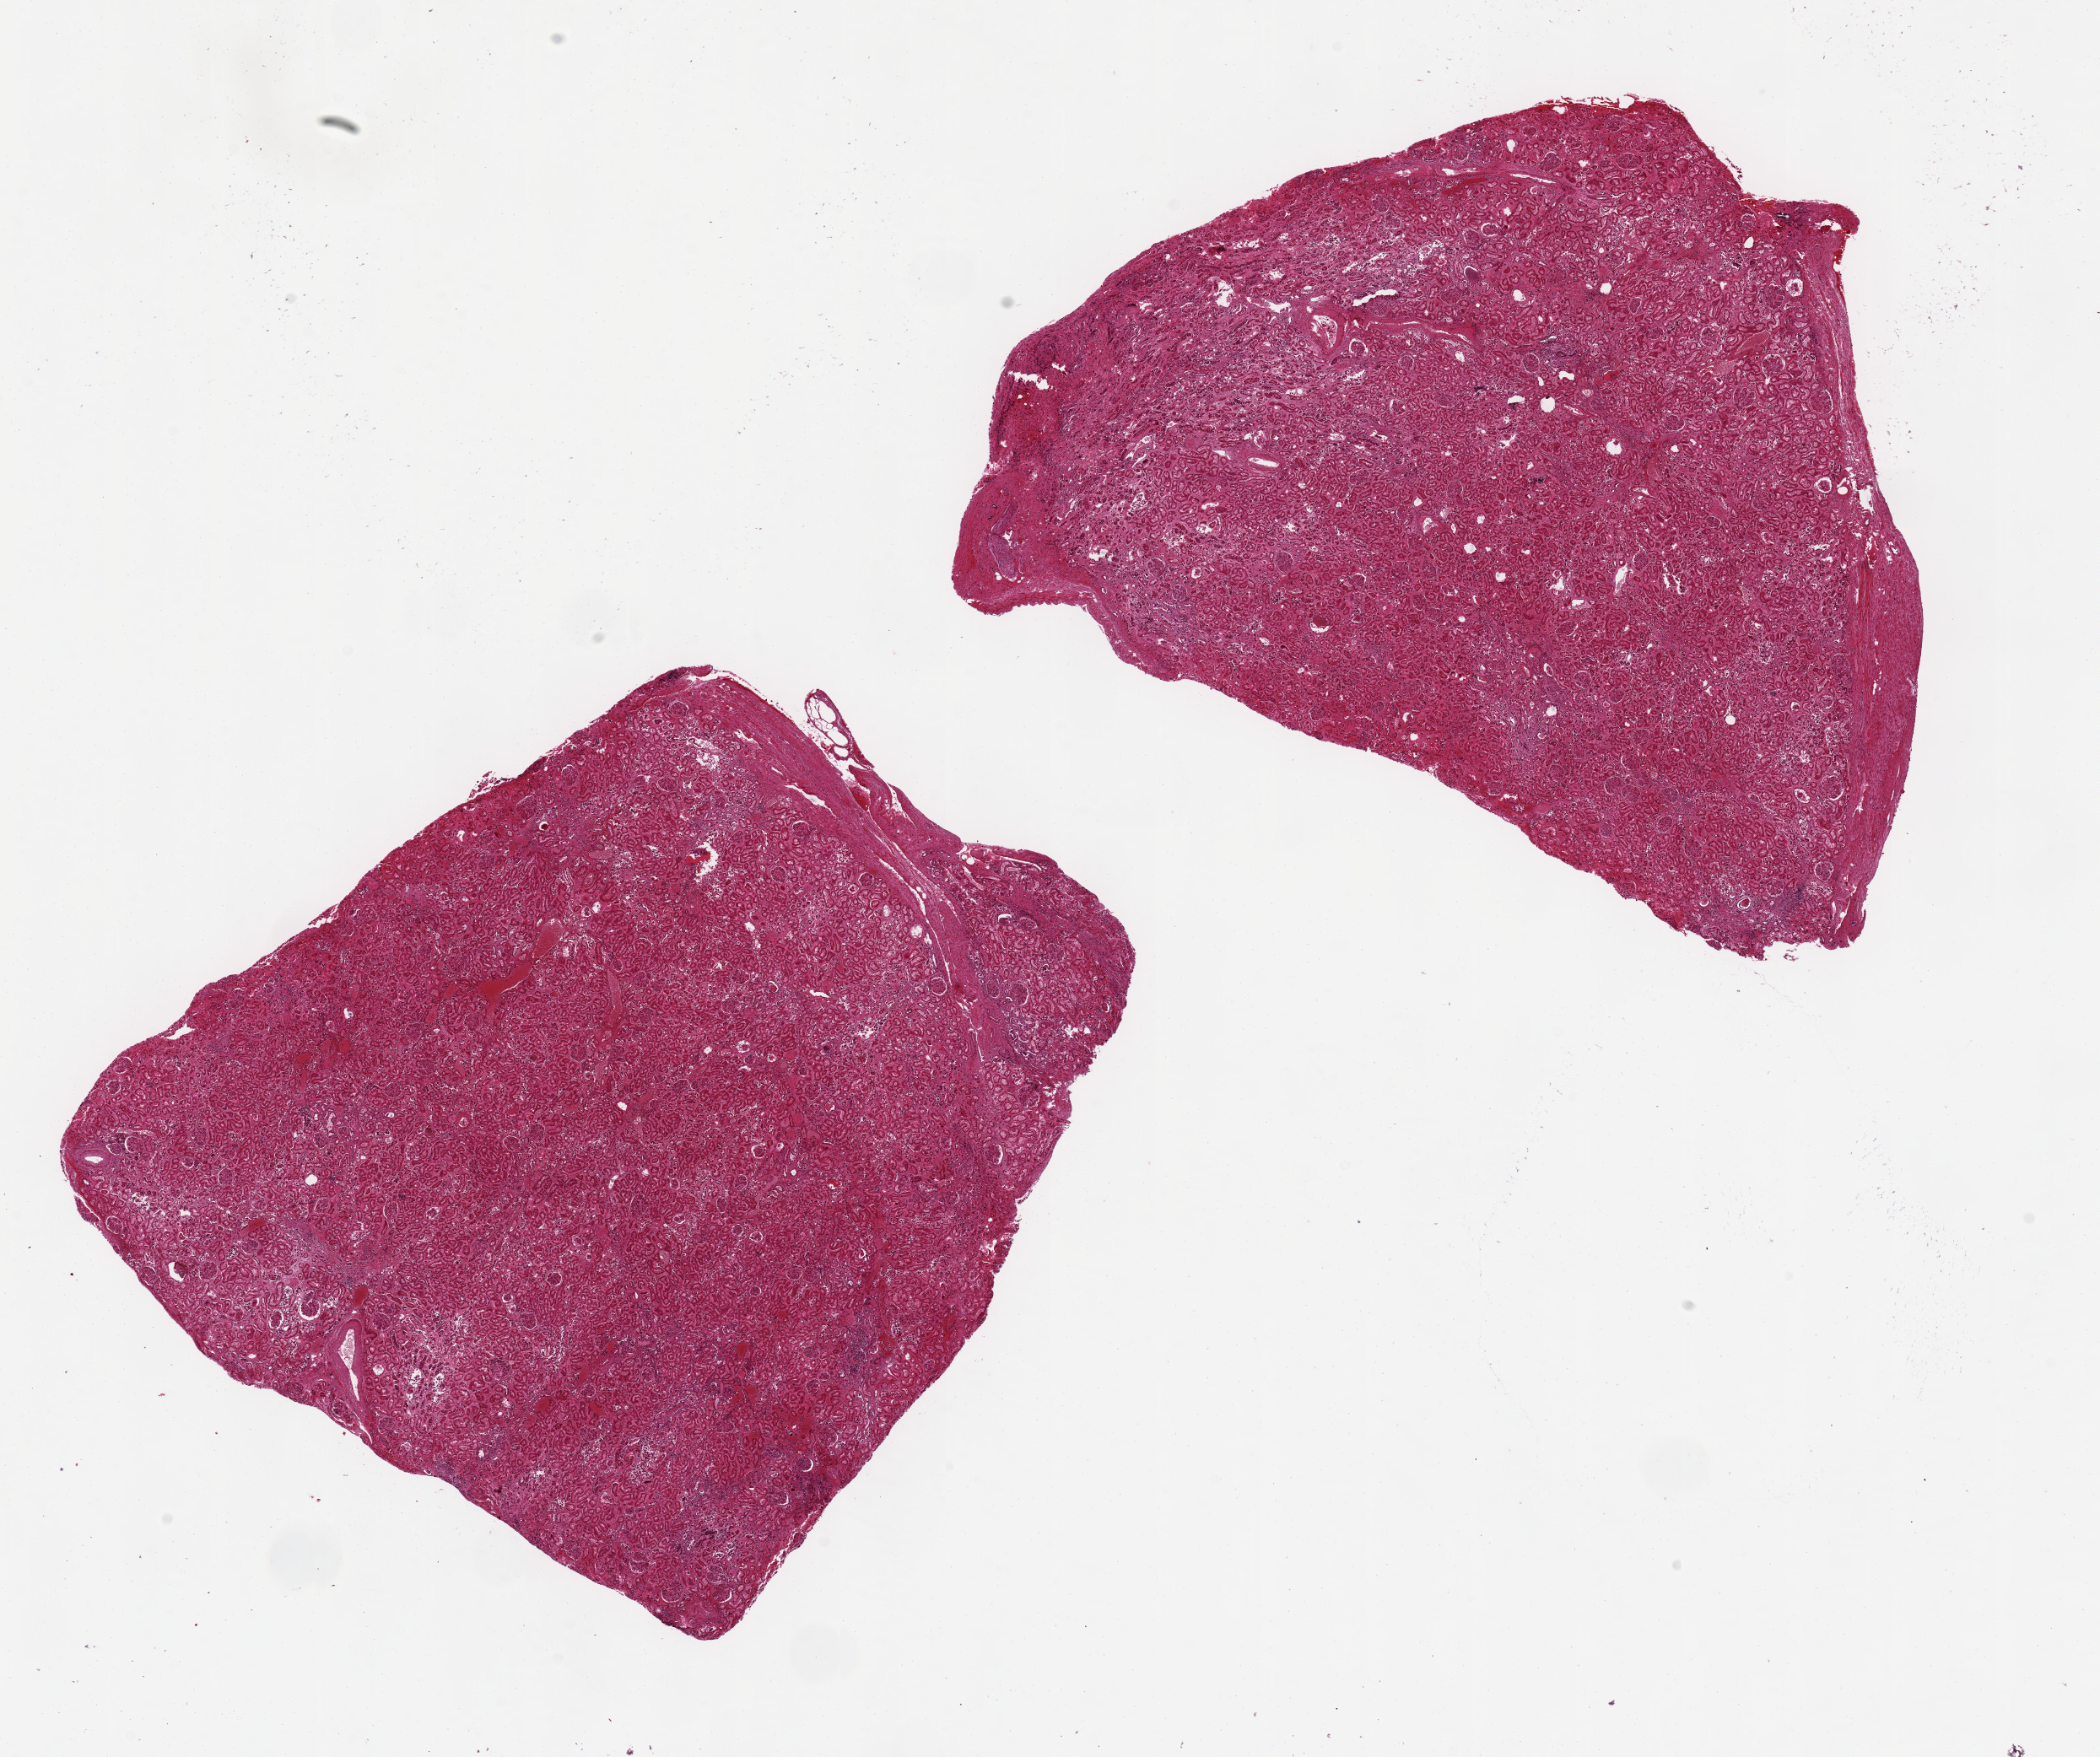
Hematoxylin and eosin (H&E) whole-slide image — shown as a low-resolution overview of the whole scanned area (about 19.7 x 16.5 mm). PAXgene-fixed, paraffin-embedded tissue. Target tissue: renal cortex. Tissue donor sample. Male donor.
Reviewer comment on this tissue sample: 2 aliquots, ~8.5x8mm. All cortex, may be used when re-labled as cortex. Tubules autolyzed, crystalloid deposits in tubular lumina.